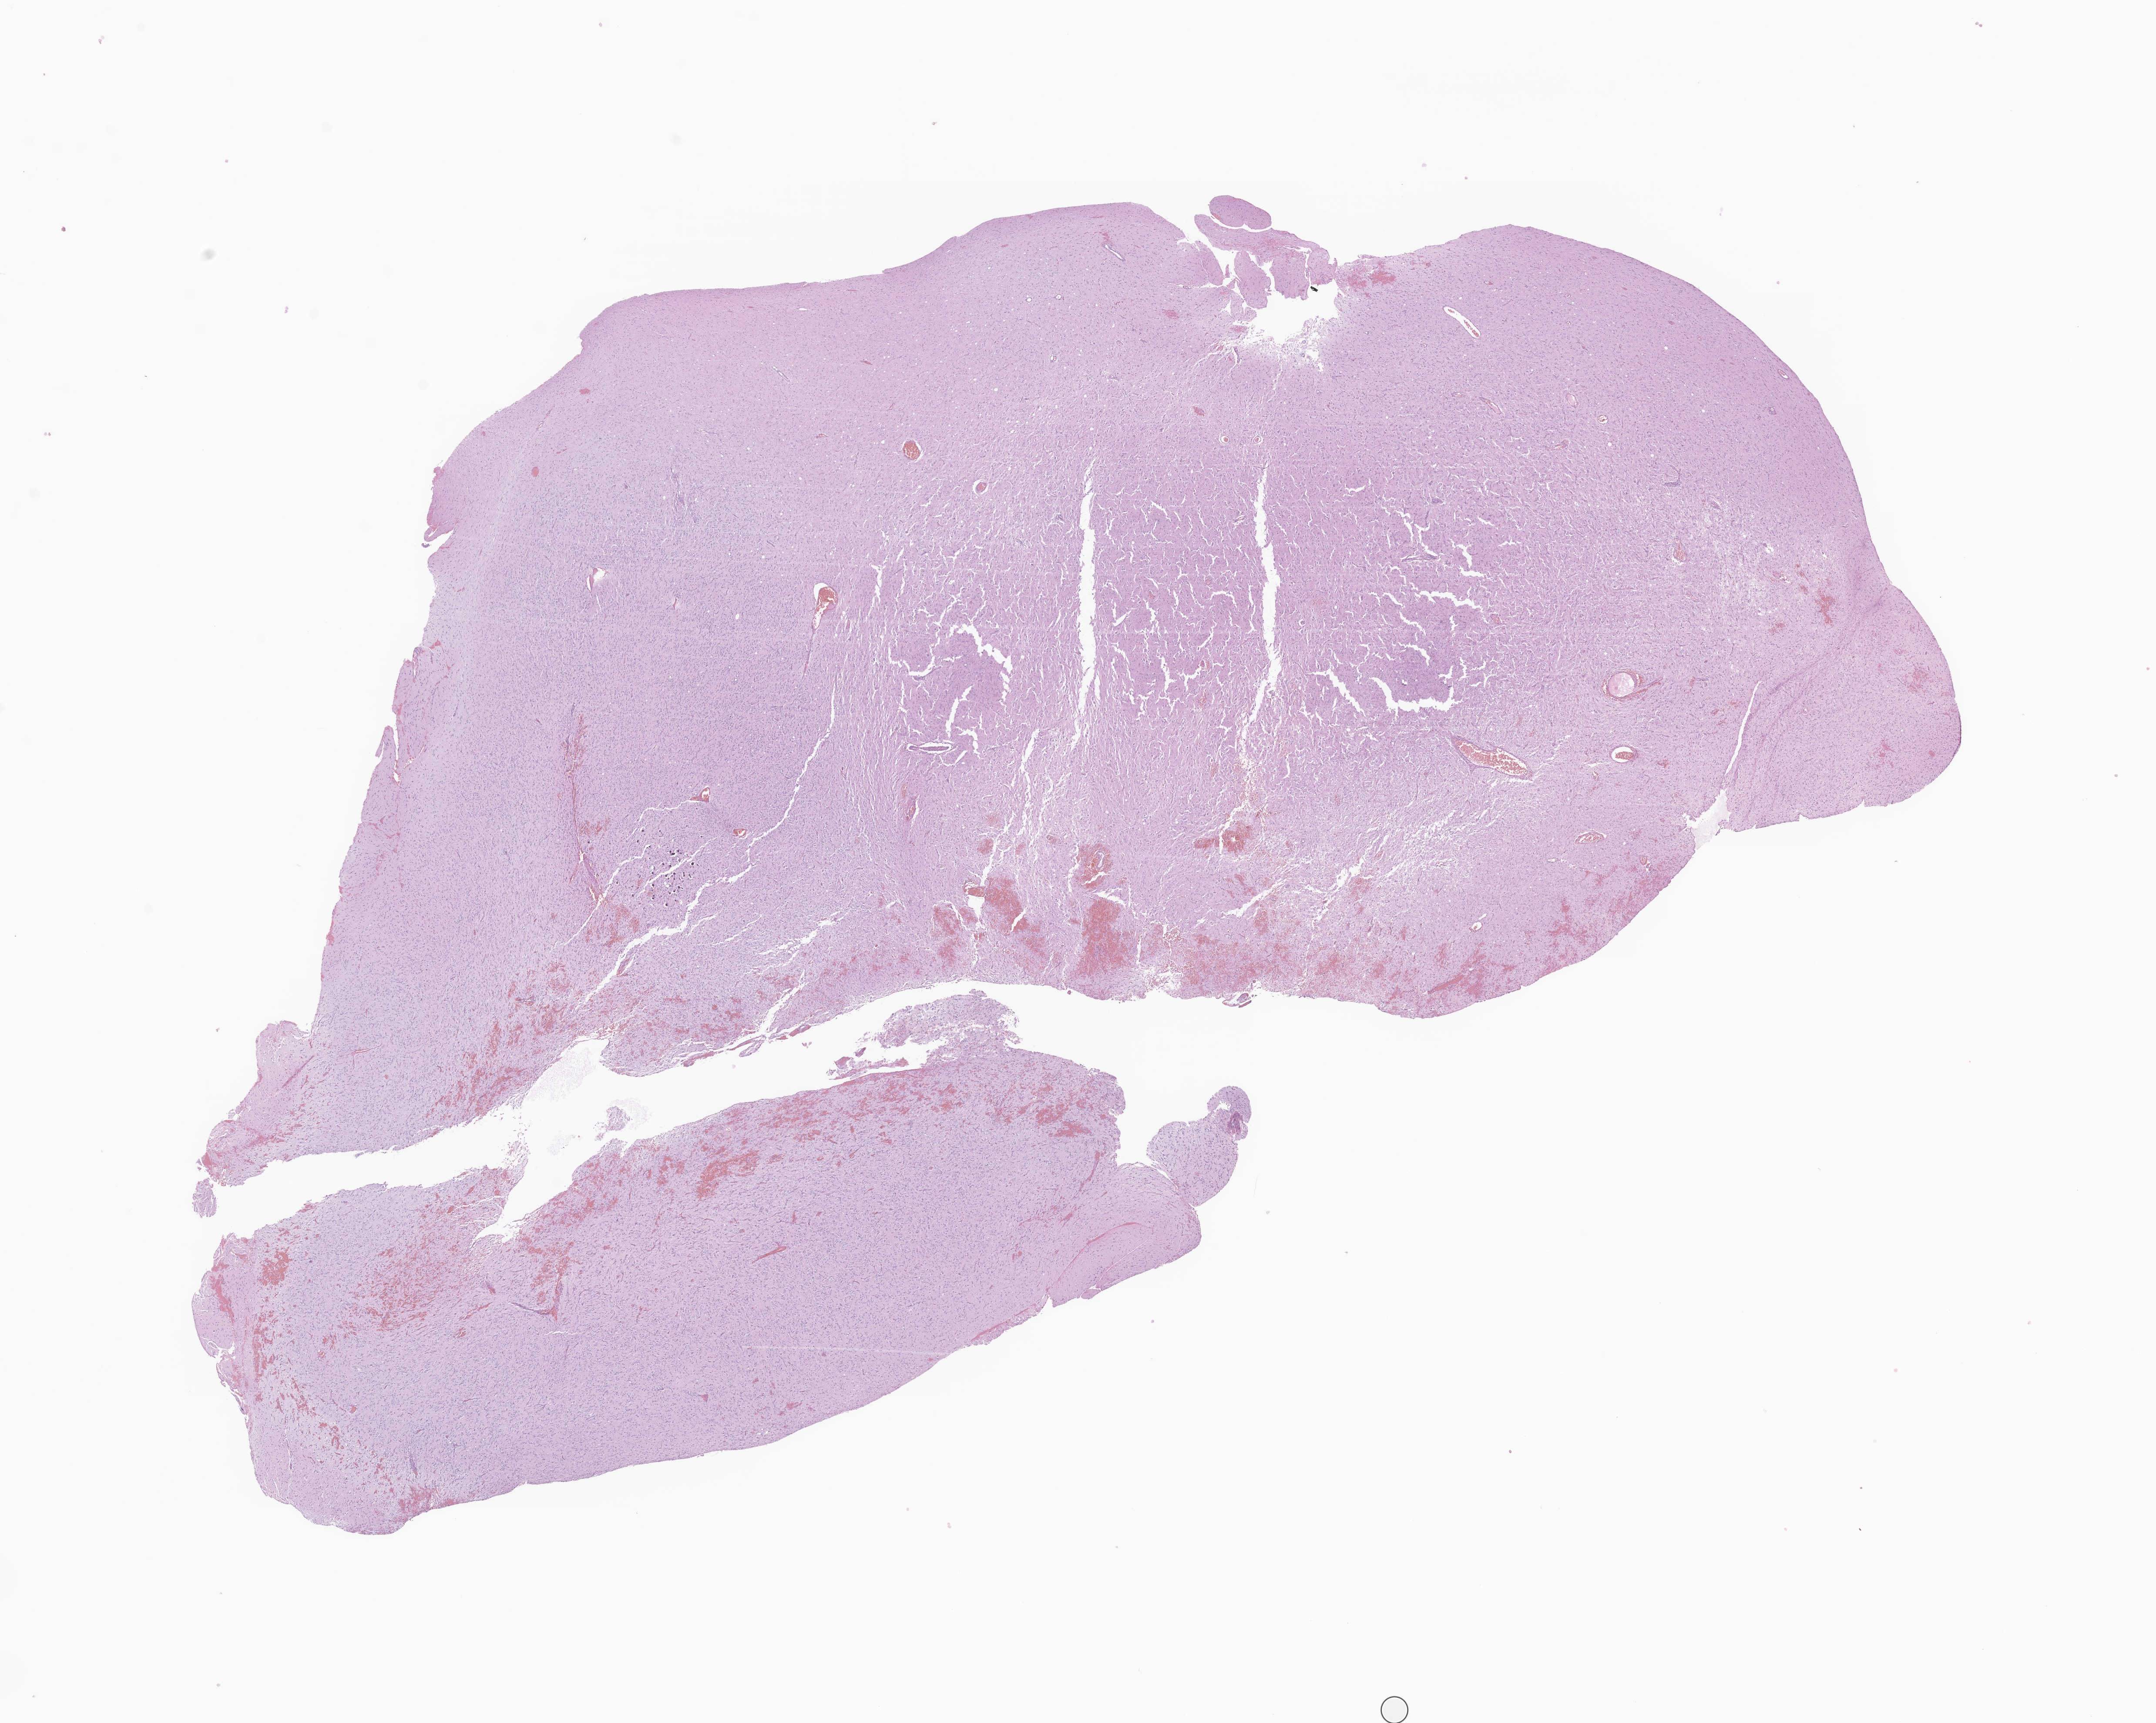
H&E whole-slide image of tumor tissue from the brain, low-resolution overview of the scanned area, about 20.9 x 16.7 mm; formalin-fixed, paraffin-embedded (FFPE) tissue. Patient male; age 58 months.
* diagnosis (ICD-O-3 morphology term): Neoplasm, benign